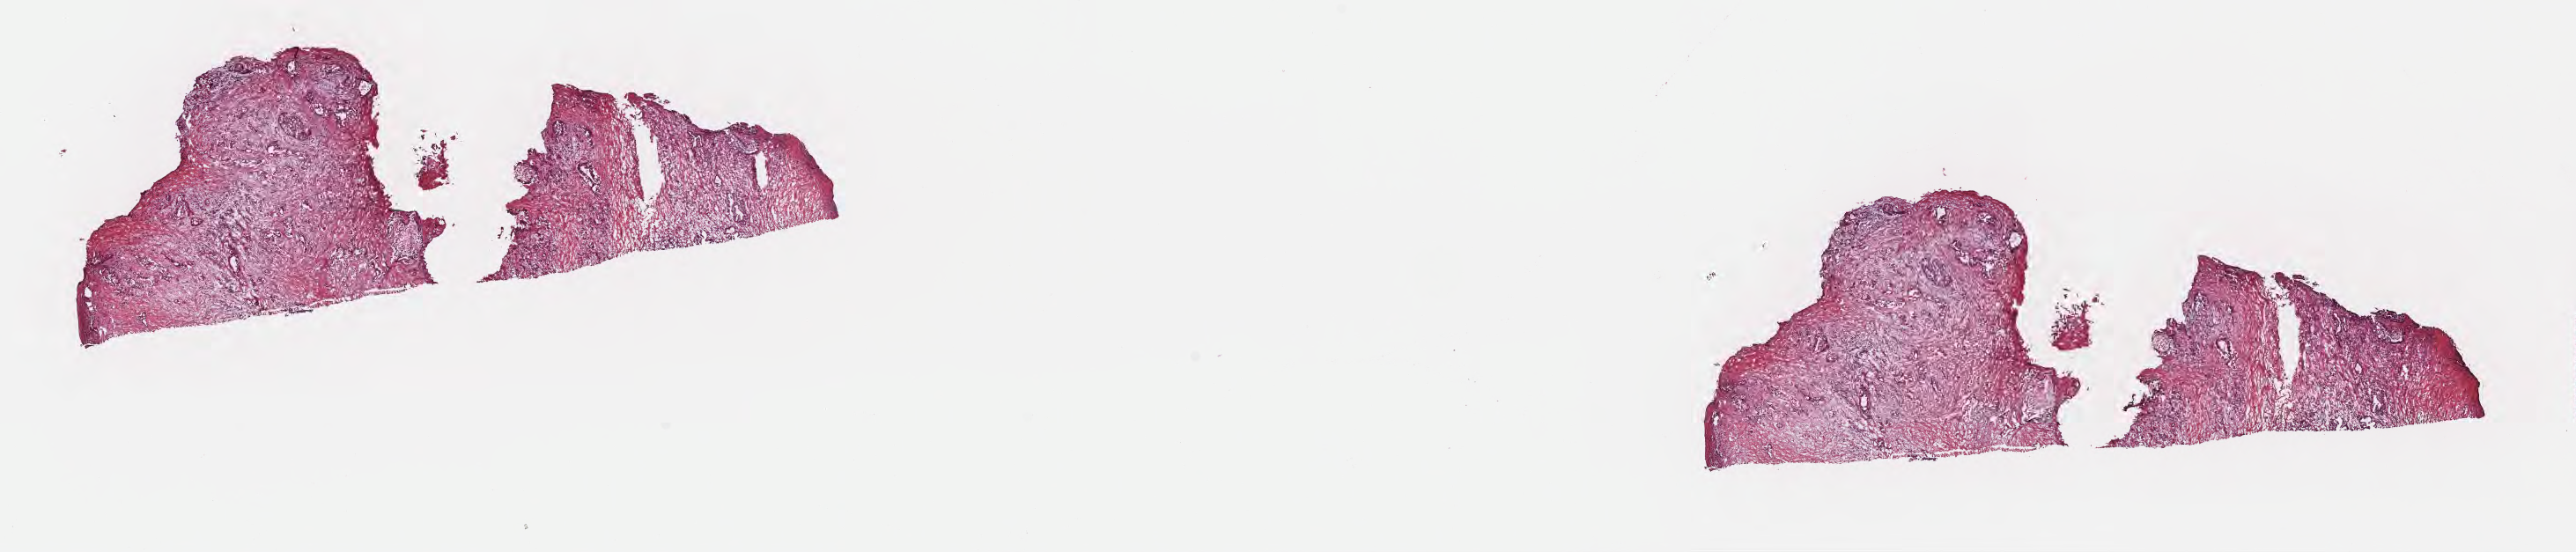
Hematoxylin and eosin (H&E) whole-slide image, low-resolution overview of the scanned area, about 23.7 x 5.1 mm, cryosection, specimen: primary tumor, anatomic site: tail of pancreas. Female, age 63 years at initial diagnosis. Tumor grade: G2 (moderately differentiated). Pathologist review of this section (percent, as recorded): tumor cells 30%, tumor nuclei 40%, stromal cells 70%, necrosis 0%, normal cells 0%. Infiltration values recorded for this section: lymphocyte infiltration 0%, monocyte infiltration 0%, neutrophil infiltration 0%.
Histologic diagnosis: Infiltrating duct carcinoma, NOS. AJCC pathologic stage: Stage III. Section: top of the tissue portion.